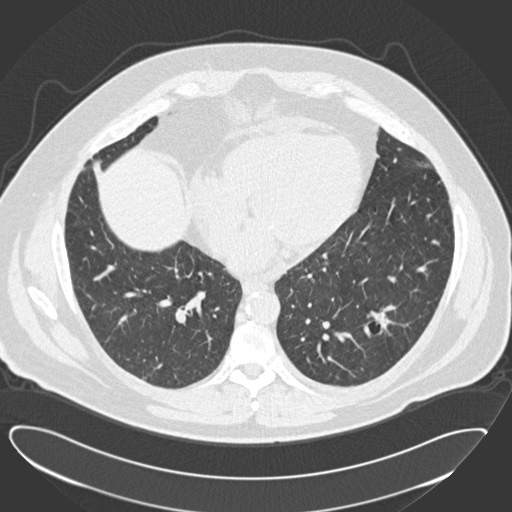
Low-dose screening chest CT, axial slice, first (baseline) screen, lung window (W 1500 / L -600 HU), standard (soft-tissue) reconstruction kernel (B30f), slice 91 of 183 in the series. Male participant, aged 57 years at enrolment. Current smoker at enrolment.
Expert-annotated lung lesion, bounding box [x1, y1, x2, y2] px = [355, 300, 408, 351]. The screening reader recorded 2 non-calcified nodules or masses ≥4 mm on this exam; which of them this box marks is not recorded. Official screen result: positive, change unspecified: nodule(s) >= 4 mm or enlarging nodule(s), mass(es), or other non-specific abnormalities suspicious for lung cancer. Lung cancer was diagnosed 791 days after this screen: squamous cell carcinoma, NOS, left lower lobe, moderately differentiated (G2), stage IA (AJCC 6th edition), 22 mm at pathology.